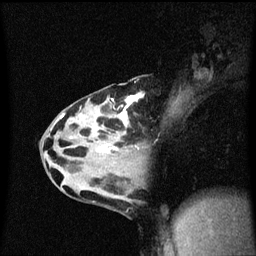
Breast MRI (dynamic contrast-enhanced), one sagittal slice; slice 28 of 60 in the series (ordered by position); dynamic contrast-enhanced series, image 2 of 3 at this slice position (ordered by acquisition); 1.5 T; TE 4.2 ms, TR 8.4 ms; 256 × 256 image matrix, field of view 200 × 200 mm. Patient: female, 32 years.
Annotated regions visible in this slice (semi-automatic segmentation, software-assisted and operator-edited):
- analysis volume of interest (the breast-tissue region the enhancement analysis was run in; not a lesion): bounding box [x1, y1, x2, y2] px = [55, 78, 177, 167]
- tumour enhancement mask (voxels above the 70 % enhancement threshold inside the analysis volume of interest): [61, 94, 145, 153]